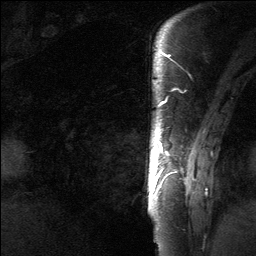
Breast MRI (dynamic contrast-enhanced), one sagittal slice; dynamic contrast-enhanced study with each time point stored as its own series, time point 2 of 3 at this slice position (early post-contrast, ordered by acquisition time); 1.5 T; TE 4.8 ms, TR 27 ms; 2 mm slice thickness; 256 × 256 image matrix, field of view 180 × 180 mm. Patient: female, 39 years. Case-level facts recorded for this patient, not image findings: setting: breast cancer imaged before/during neoadjuvant chemotherapy; receptor status: HER2-positive.
Annotated regions visible in this slice (semi-automatically segmented with operator editing):
- analysis volume of interest (the breast-tissue region the enhancement analysis was run in; not a lesion): bounding box [x1, y1, x2, y2] px = [147, 40, 201, 217]
- tumour enhancement mask (voxels above the 90 % enhancement threshold inside the analysis volume of interest): [150, 52, 170, 193]